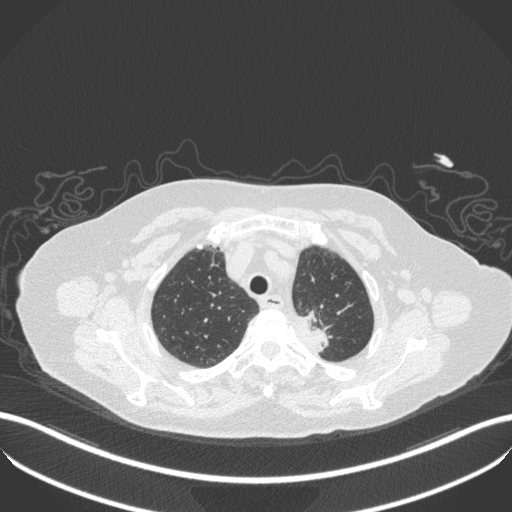
Chest CT, one axial slice; slice 282 of 353 in the series (ordered by position); reconstruction kernel B31f; lung window (W 1500 / L -600 HU); 512 × 512 image matrix. Patient: female, 81 years. Case-level facts recorded for this patient, not image findings: clinical TNM (as recorded): T2a N0 M0.
Outlined on this slice (bounding box drawn by a radiologist):
- lung tumour (recorded histology: adenocarcinoma): bounding box <286,307,330,354> (left, top, right, bottom; pixels)